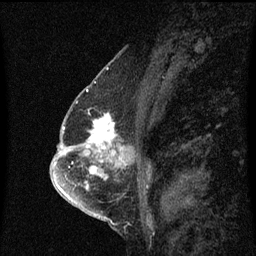
Breast MRI (dynamic contrast-enhanced), one sagittal slice; slice 36 of 60 in the series (ordered by position); dynamic contrast-enhanced series, image 2 of 3 at this slice position (ordered by acquisition); 1.5 T; TE 4.2 ms, TR 8.4 ms; 256 × 256 image matrix, field of view 200 × 200 mm. Female patient, age 57 years. Case-level facts recorded for this patient, not image findings: setting: breast cancer imaged before/during neoadjuvant chemotherapy; receptor status: HR-positive, HER2-negative.
Structures marked on this image (semi-automatic segmentation, software-assisted and operator-edited):
- analysis volume of interest (the breast-tissue region the enhancement analysis was run in; not a lesion): bounding box [x1, y1, x2, y2] px = [86, 114, 116, 145]
- tumour enhancement mask (voxels above the 70 % enhancement threshold inside the analysis volume of interest): [88, 114, 116, 145]